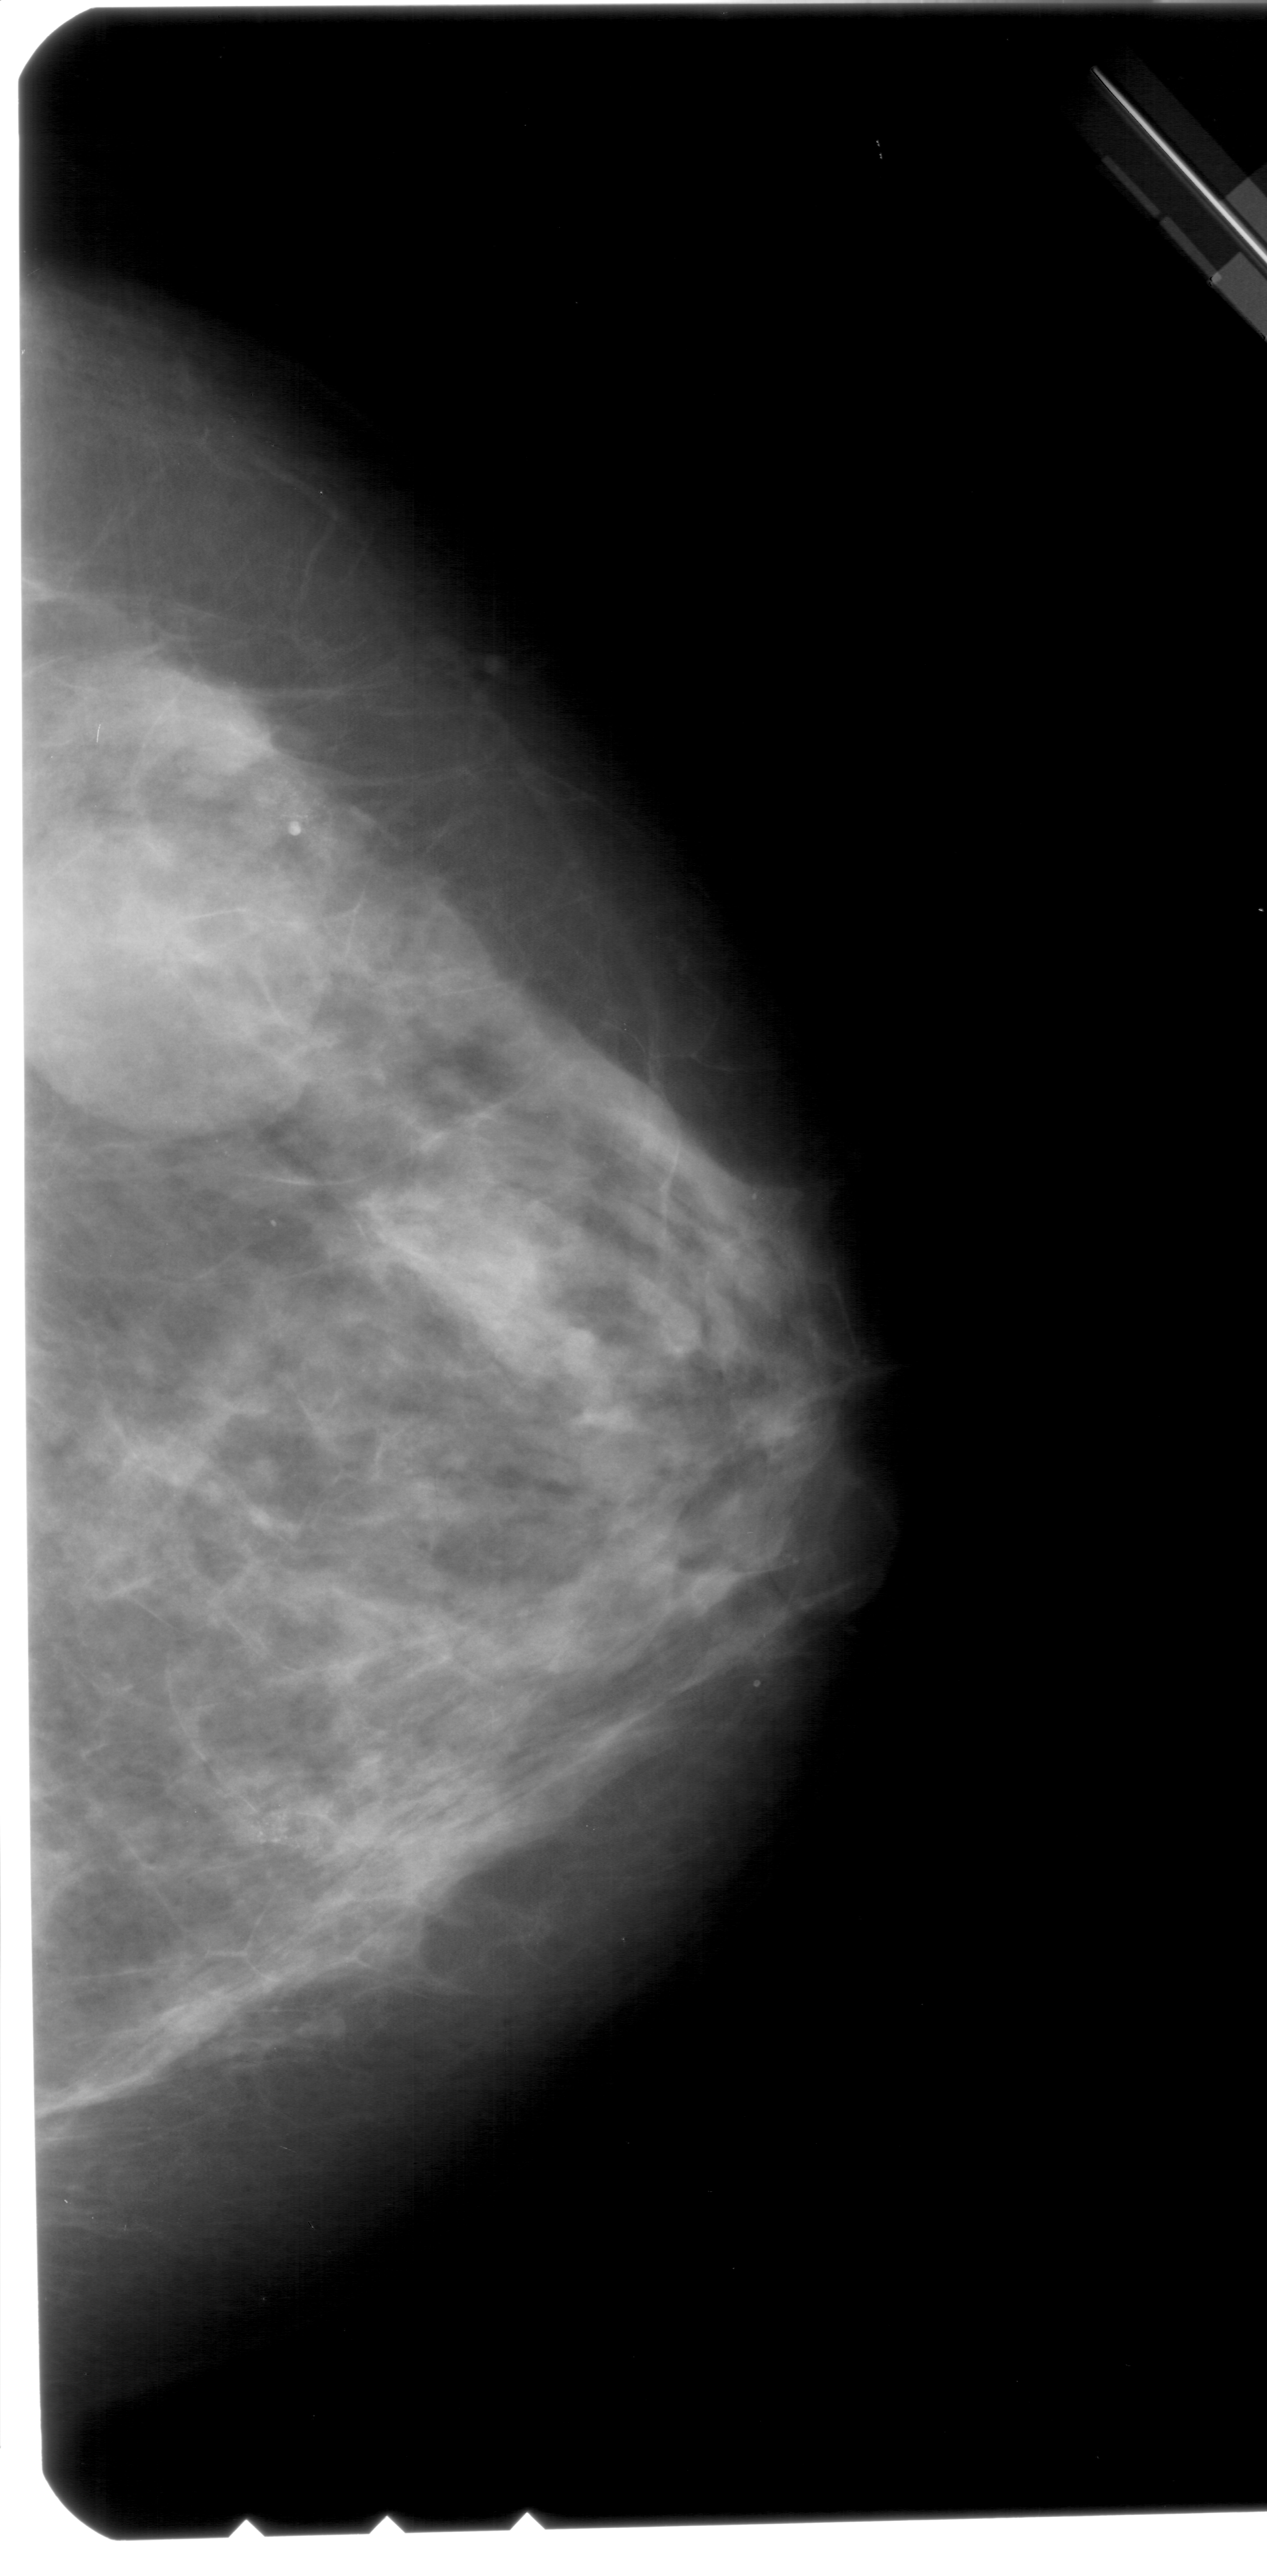
Digitized screen-film mammogram, right breast, CC view, BI-RADS breast density category 3 (scale 1–4).
Marked findings (only marked abnormalities are described; nothing is implied about the rest of the image): calcifications, morphology pleomorphic, distribution clustered; BI-RADS assessment category 4; subtlety rating 2 on a 1 (subtle) to 5 (obvious) scale; pathology result (as recorded, not read from the image): benign.